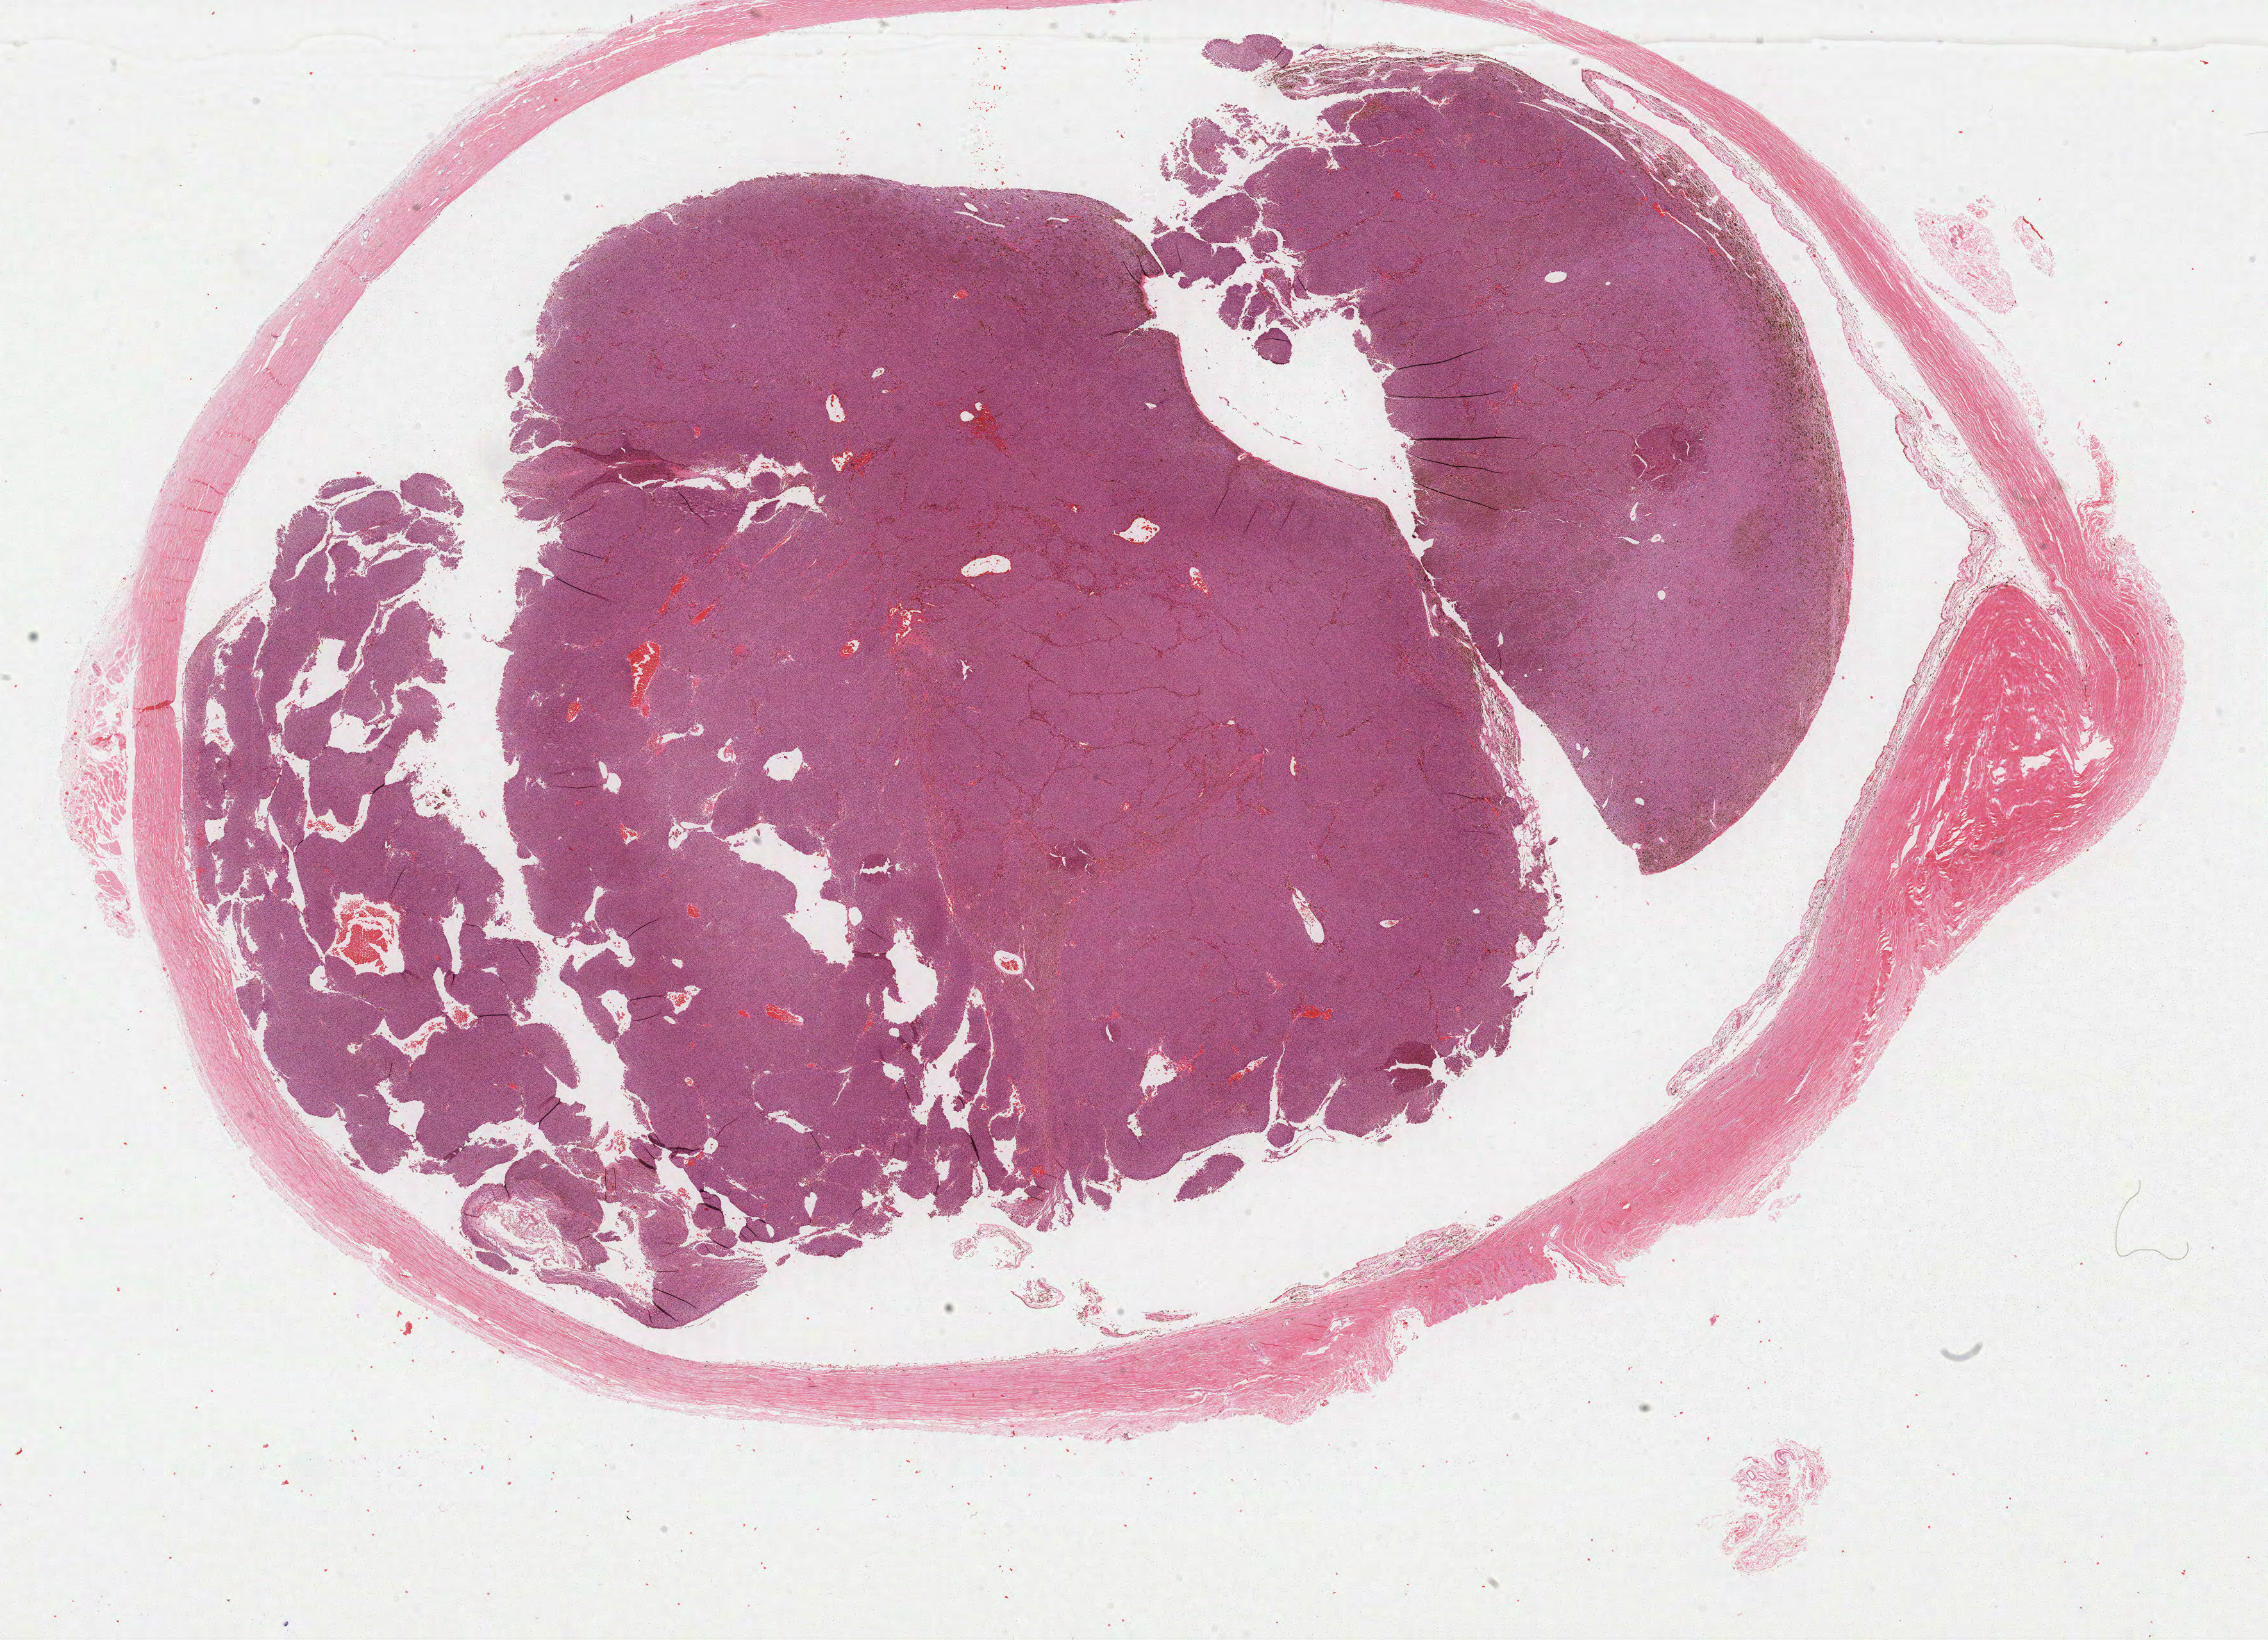
Hematoxylin and eosin (H&E) stained whole-slide image — a low-resolution overview of the entire scanned area, about 28.0 x 20.2 mm, formalin-fixed paraffin-embedded (FFPE) diagnostic section, uvea, primary tumour sample. Female, age 50 years at initial diagnosis.
AJCC pathologic stage: IIB (7th edition). Laterality: left. Histologic diagnosis: Mixed epithelioid and spindle cell melanoma.